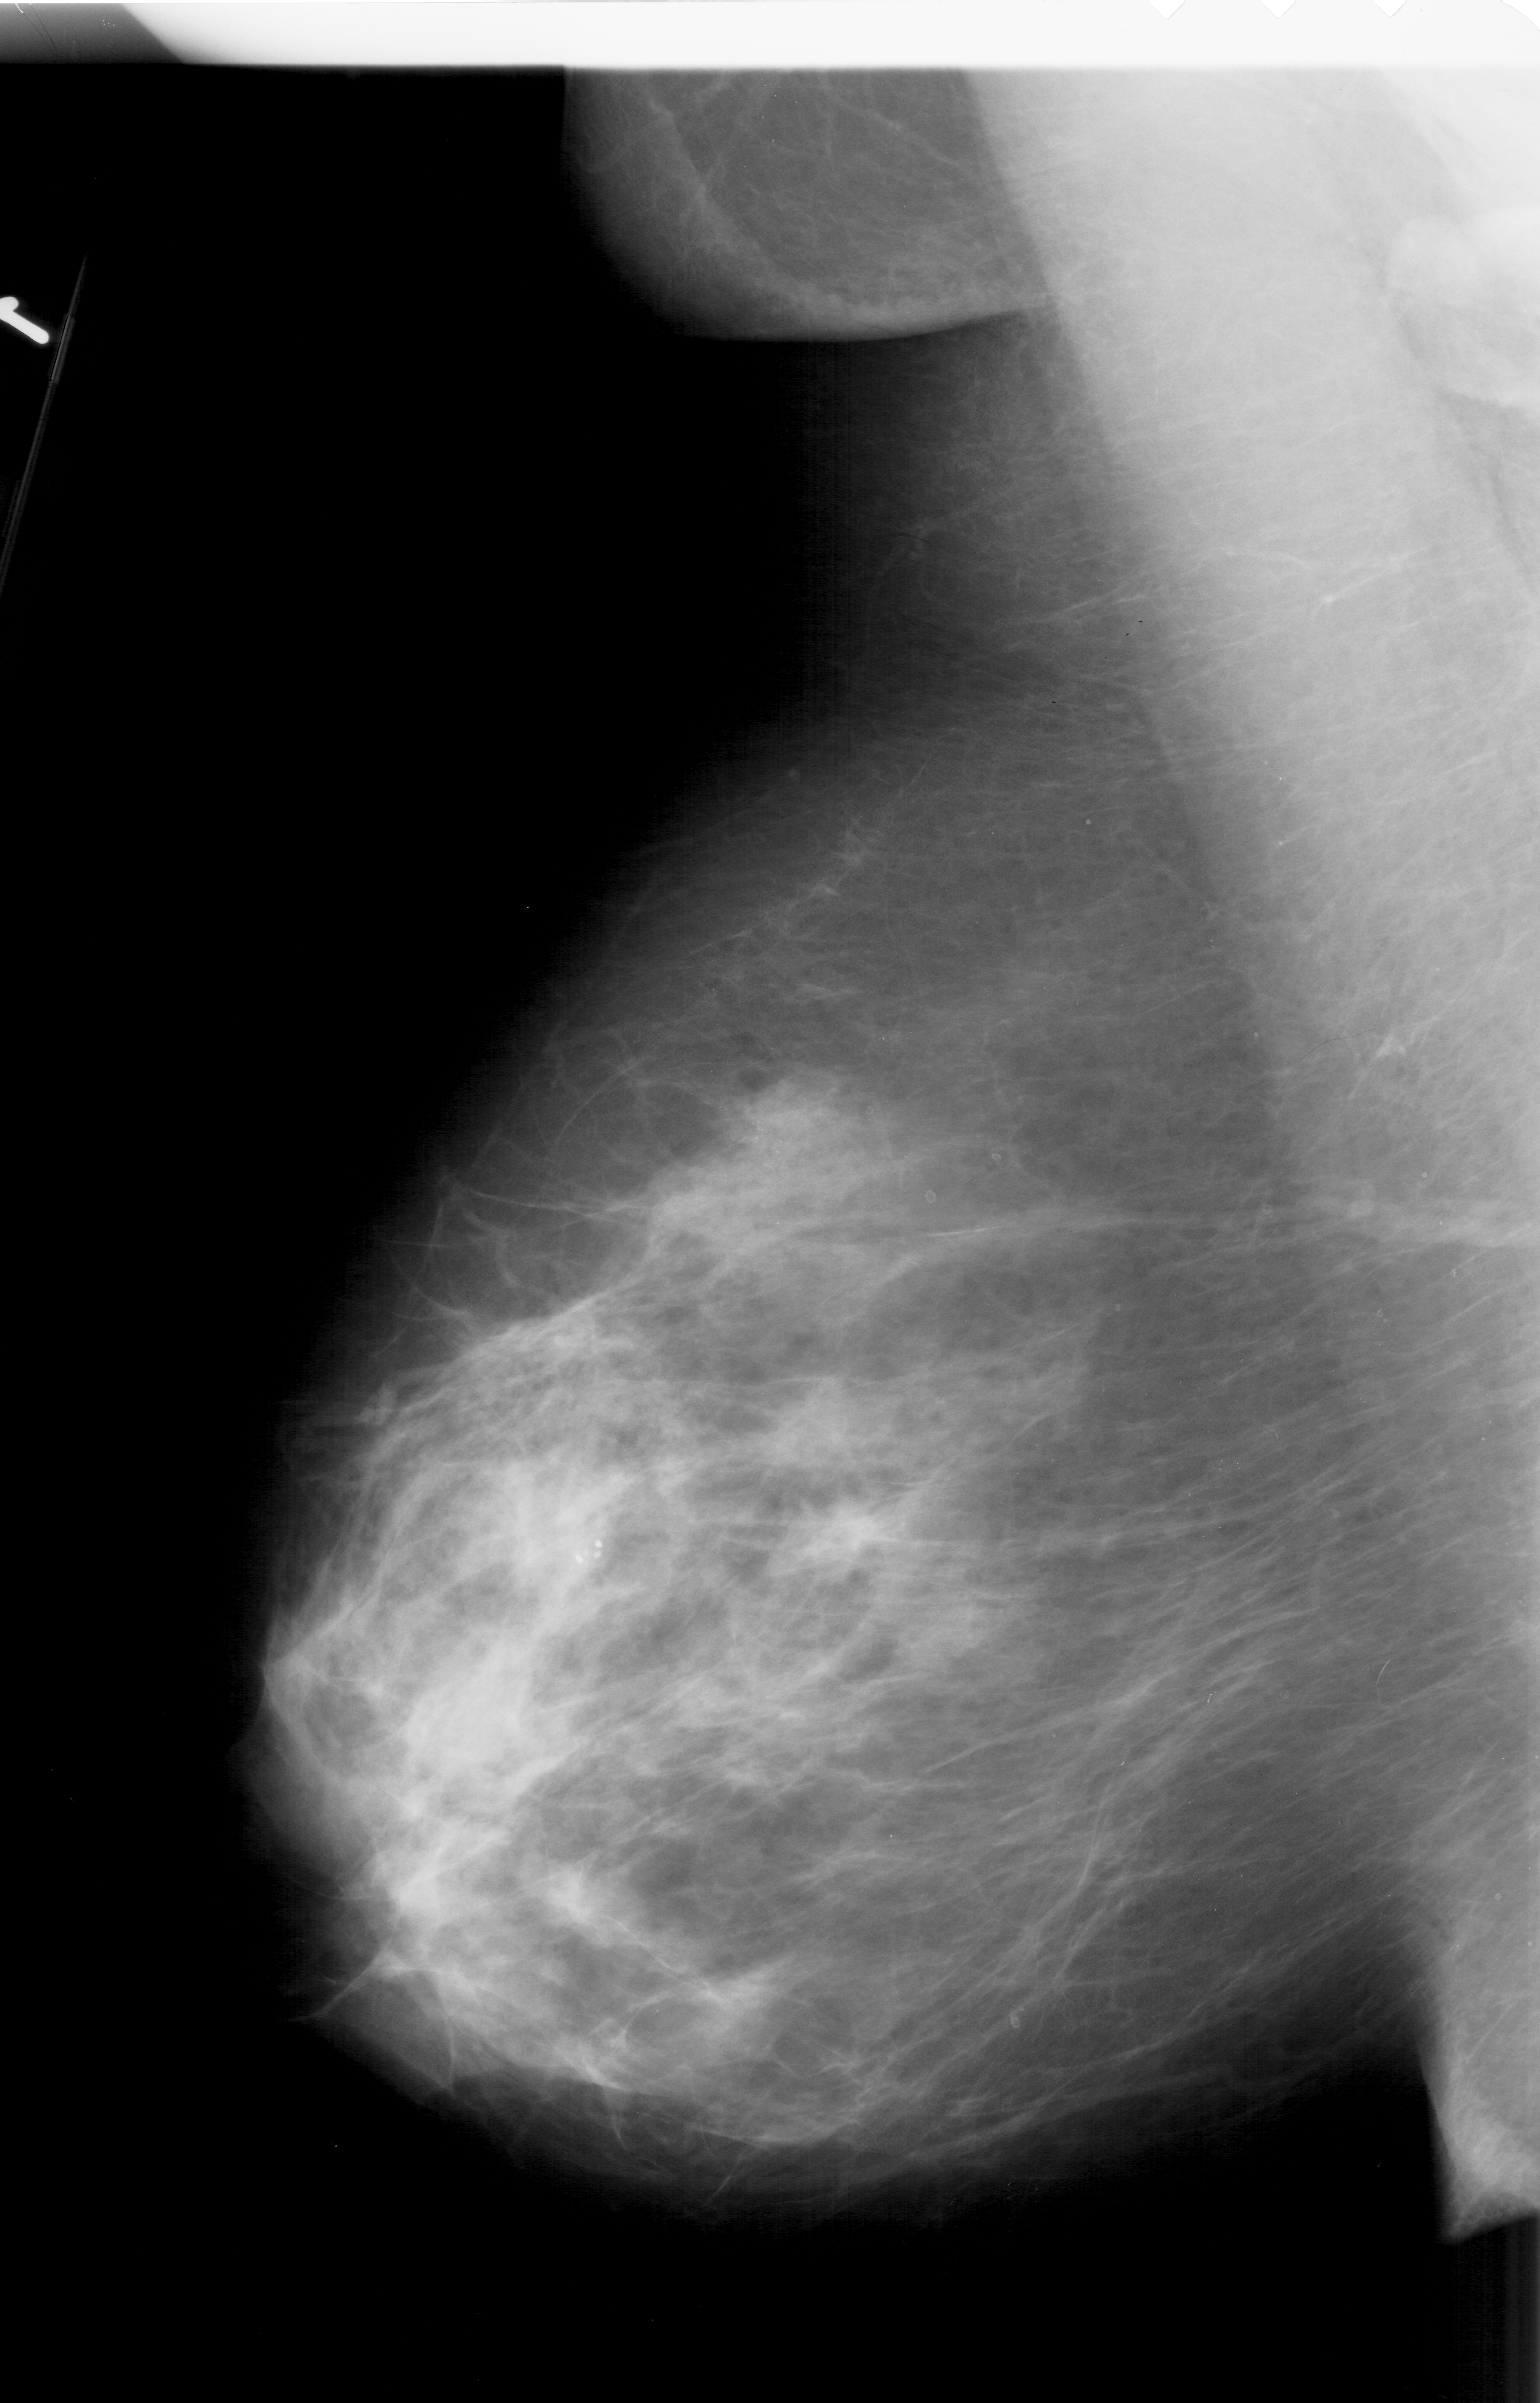
Digitized screen-film mammogram. Left breast. Mediolateral oblique (MLO) view. Breast composition: extremely dense (BI-RADS density category 4 of 4). 1540 × 2403 image matrix.
Expert-marked regions of interest on this film, with their recorded descriptors:
- calcifications, morphology pleomorphic, distribution clustered; BI-RADS assessment category 4; subtlety rating 2 on a 1 (subtle) to 5 (obvious) scale; pathology (as recorded): malignant: bounding box <710,1096,804,1191> (left, top, right, bottom; pixels)